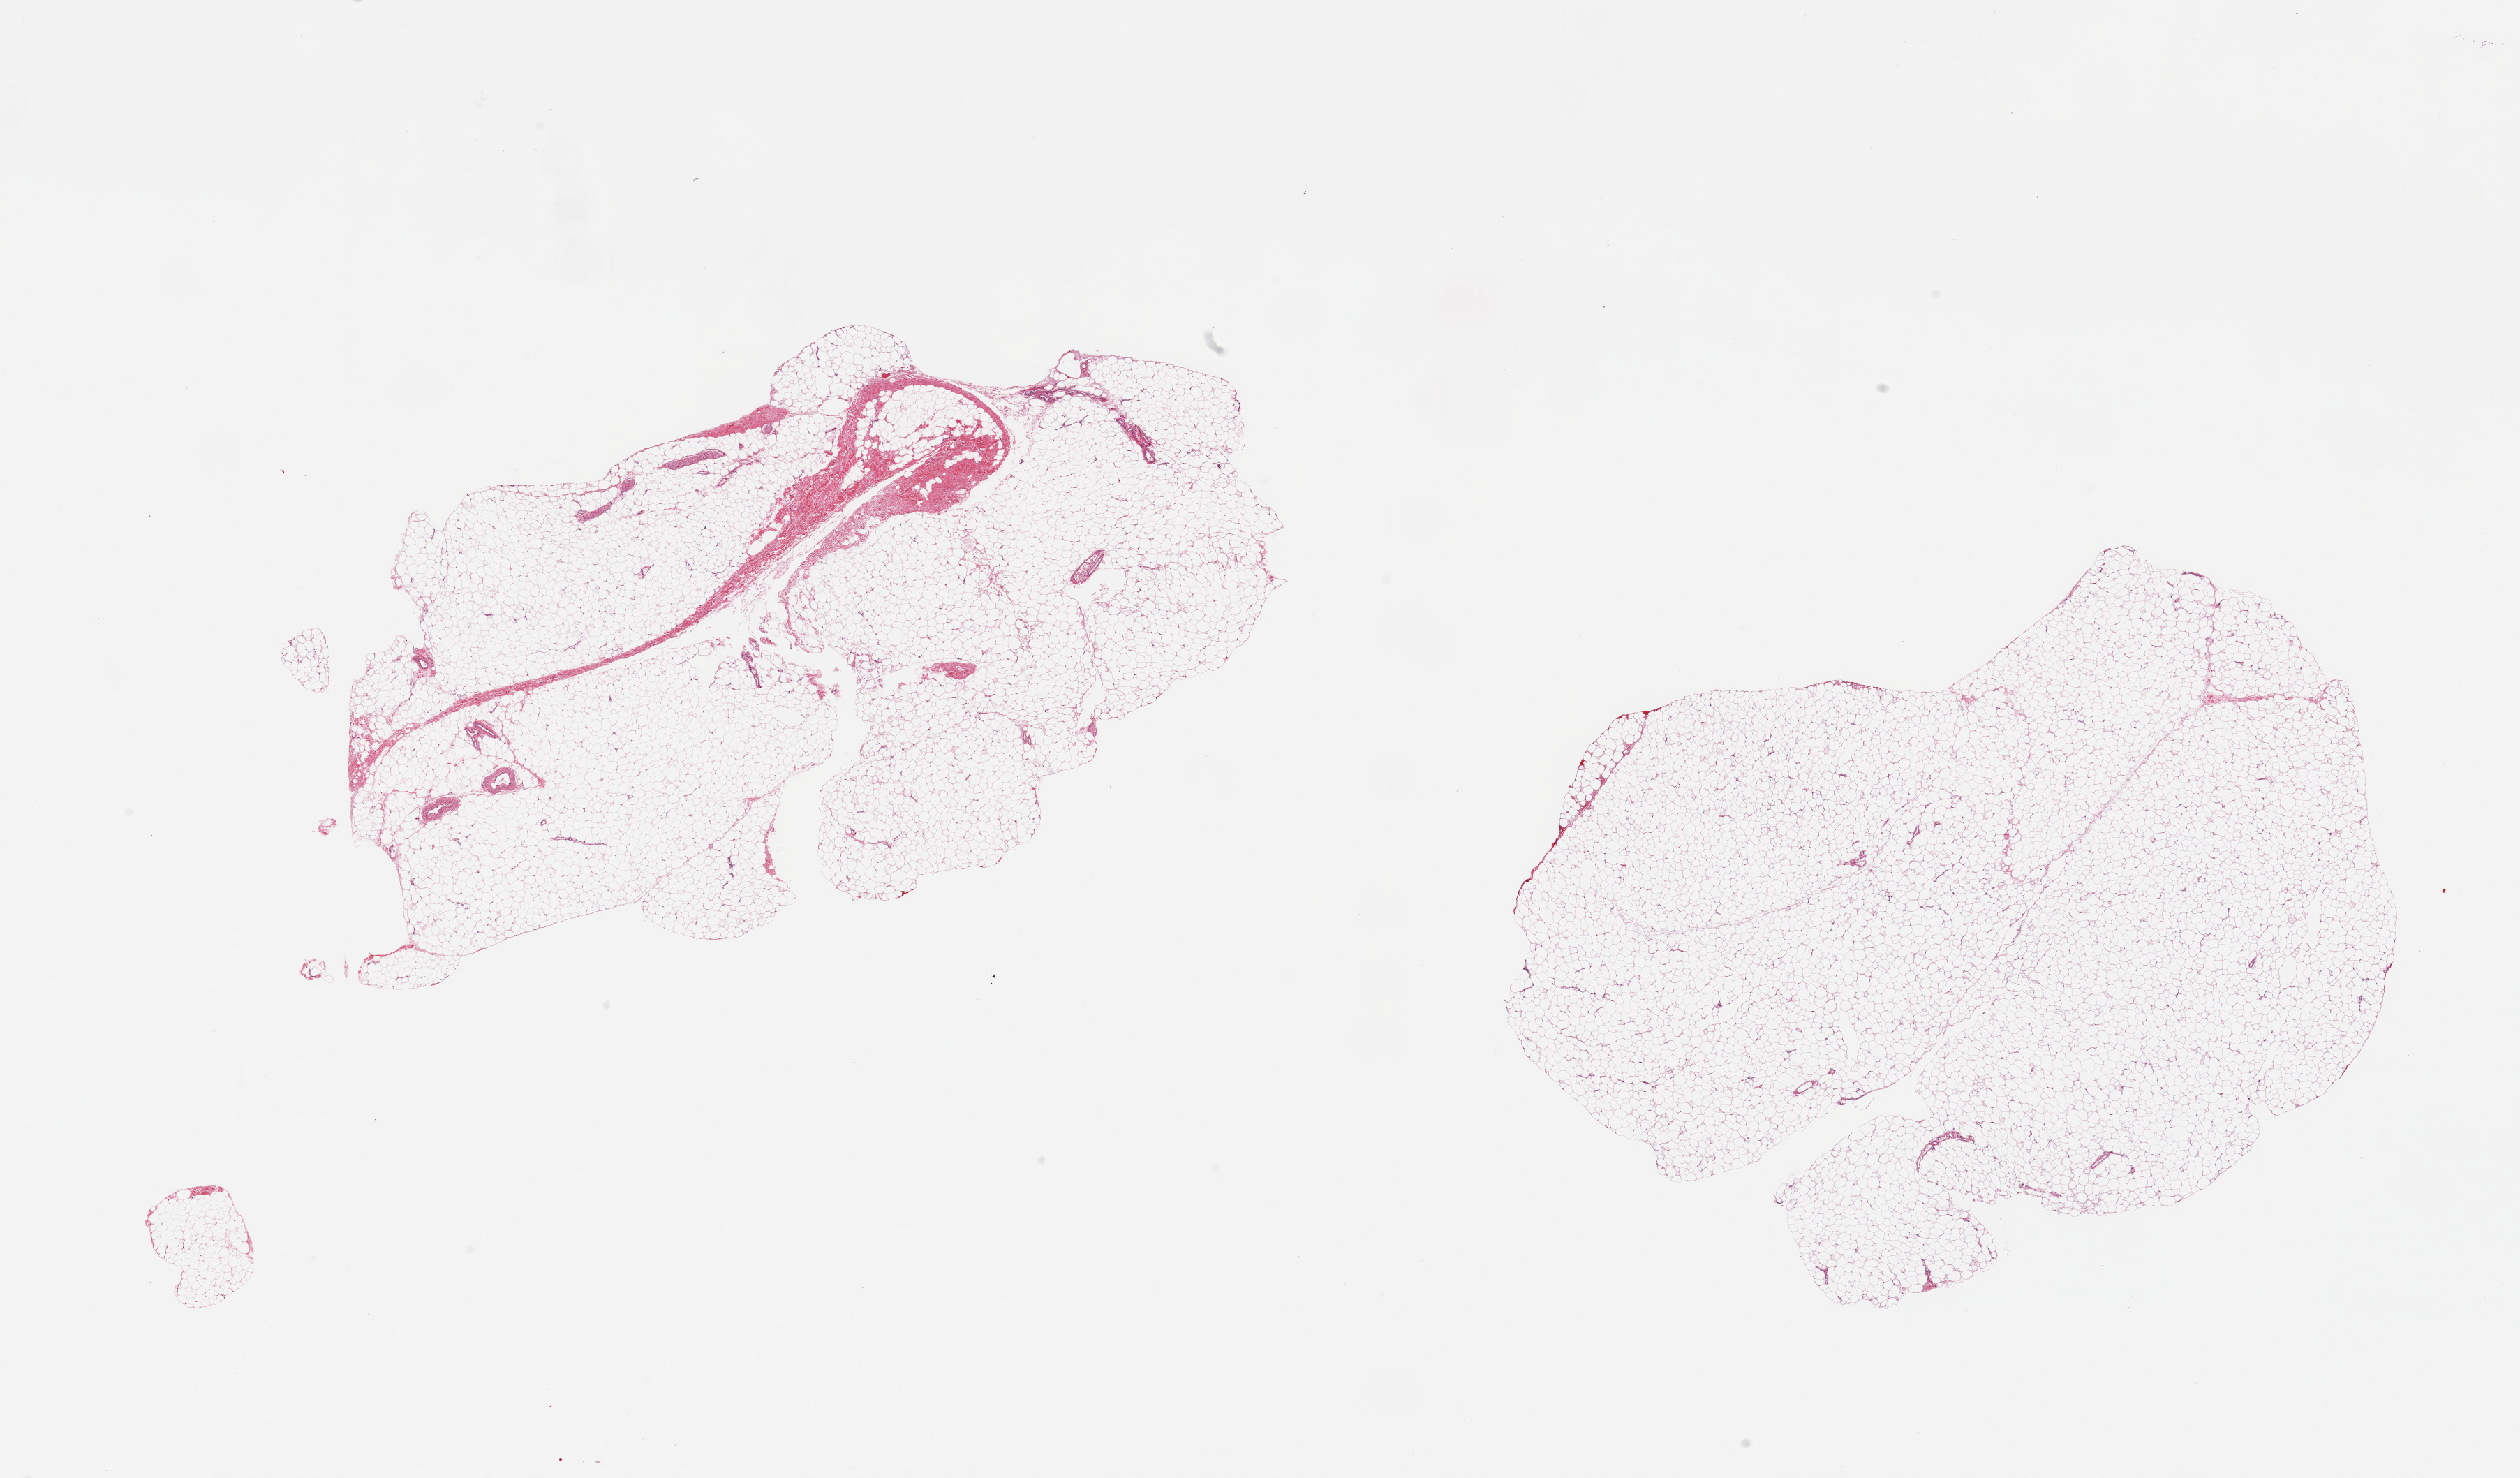
Hematoxylin and eosin (H&E) whole-slide image, brightfield, low-resolution overview of the scanned area, about 28.5 x 16.7 mm (from a 20x scan); PAXgene-fixed, paraffin-embedded tissue; sampled site (target tissue): breast; tissue donor sample. Donor sex: male.
Review note (as recorded): 2 pieces; adipose tissue with 10% fibrovascular content in 1 piece; no mammary ducts.